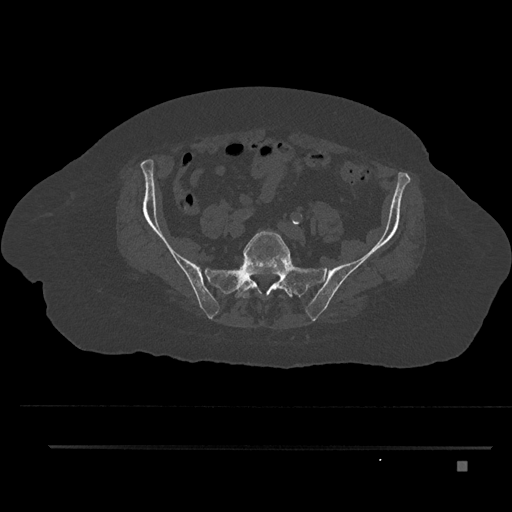
CT including the spine, one axial slice; position 16 of 797 along the scan axis; reconstruction kernel Br40s/3; 120 kVp; bone window (W 1800 / L 400 HU); 0.5 mm slice thickness; 512 × 512 image matrix, field of view 437 × 437 mm. Female patient, age 76 years. From the clinical record (not read from this slice): primary cancer: lung.
Outlined on this slice (semi-automatically segmented with operator editing):
- L5 vertebra: bounding box <242,231,290,299> (left, top, right, bottom; pixels)